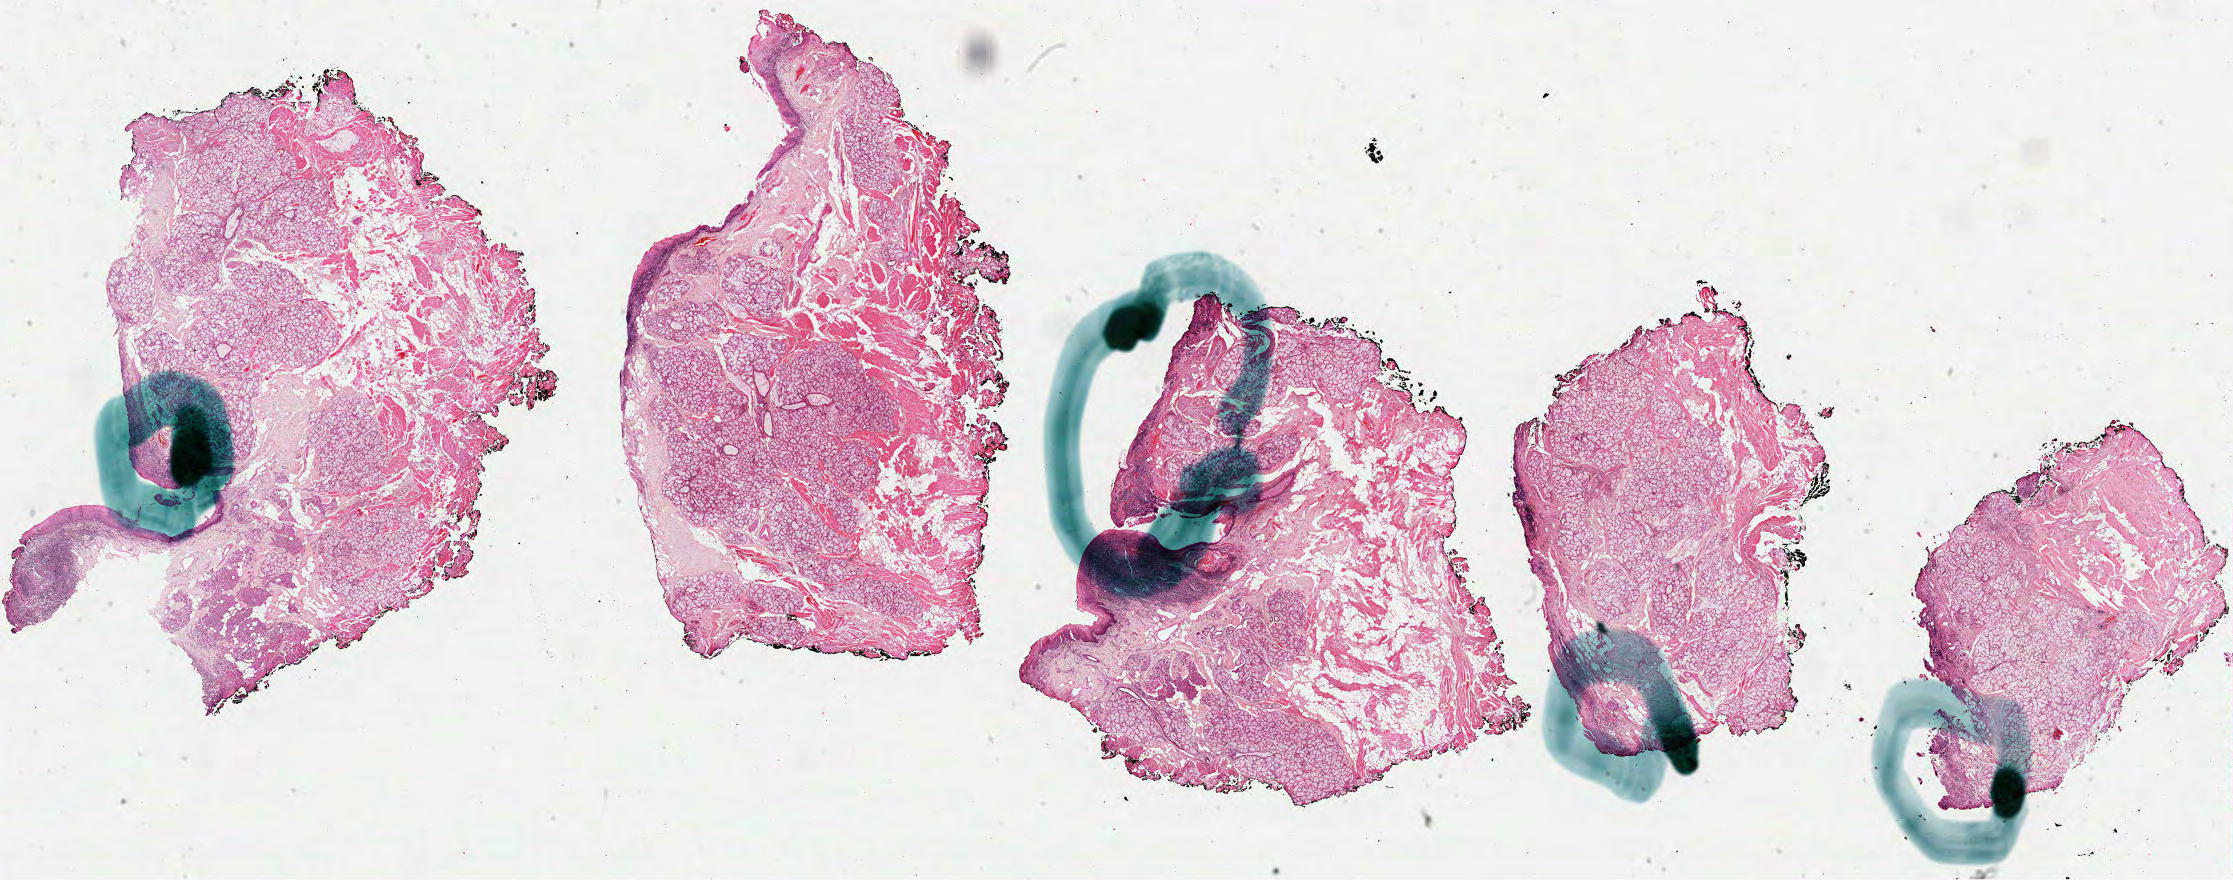
Hematoxylin and eosin (H&E) stained whole-slide image — shown as a low-resolution overview of the whole scanned area (about 36.0 x 14.2 mm, from a 40x scan); formalin-fixed paraffin-embedded (FFPE) diagnostic section; head and neck, primary tumour sample. Patient: female, age at initial diagnosis 64 years. Histologic grade: G2 (moderately differentiated).
* AJCC pathologic stage: IVA (7th edition)
* TNM: T4a N2c
* histologic diagnosis: Squamous cell carcinoma, NOS (base of tongue, NOS)